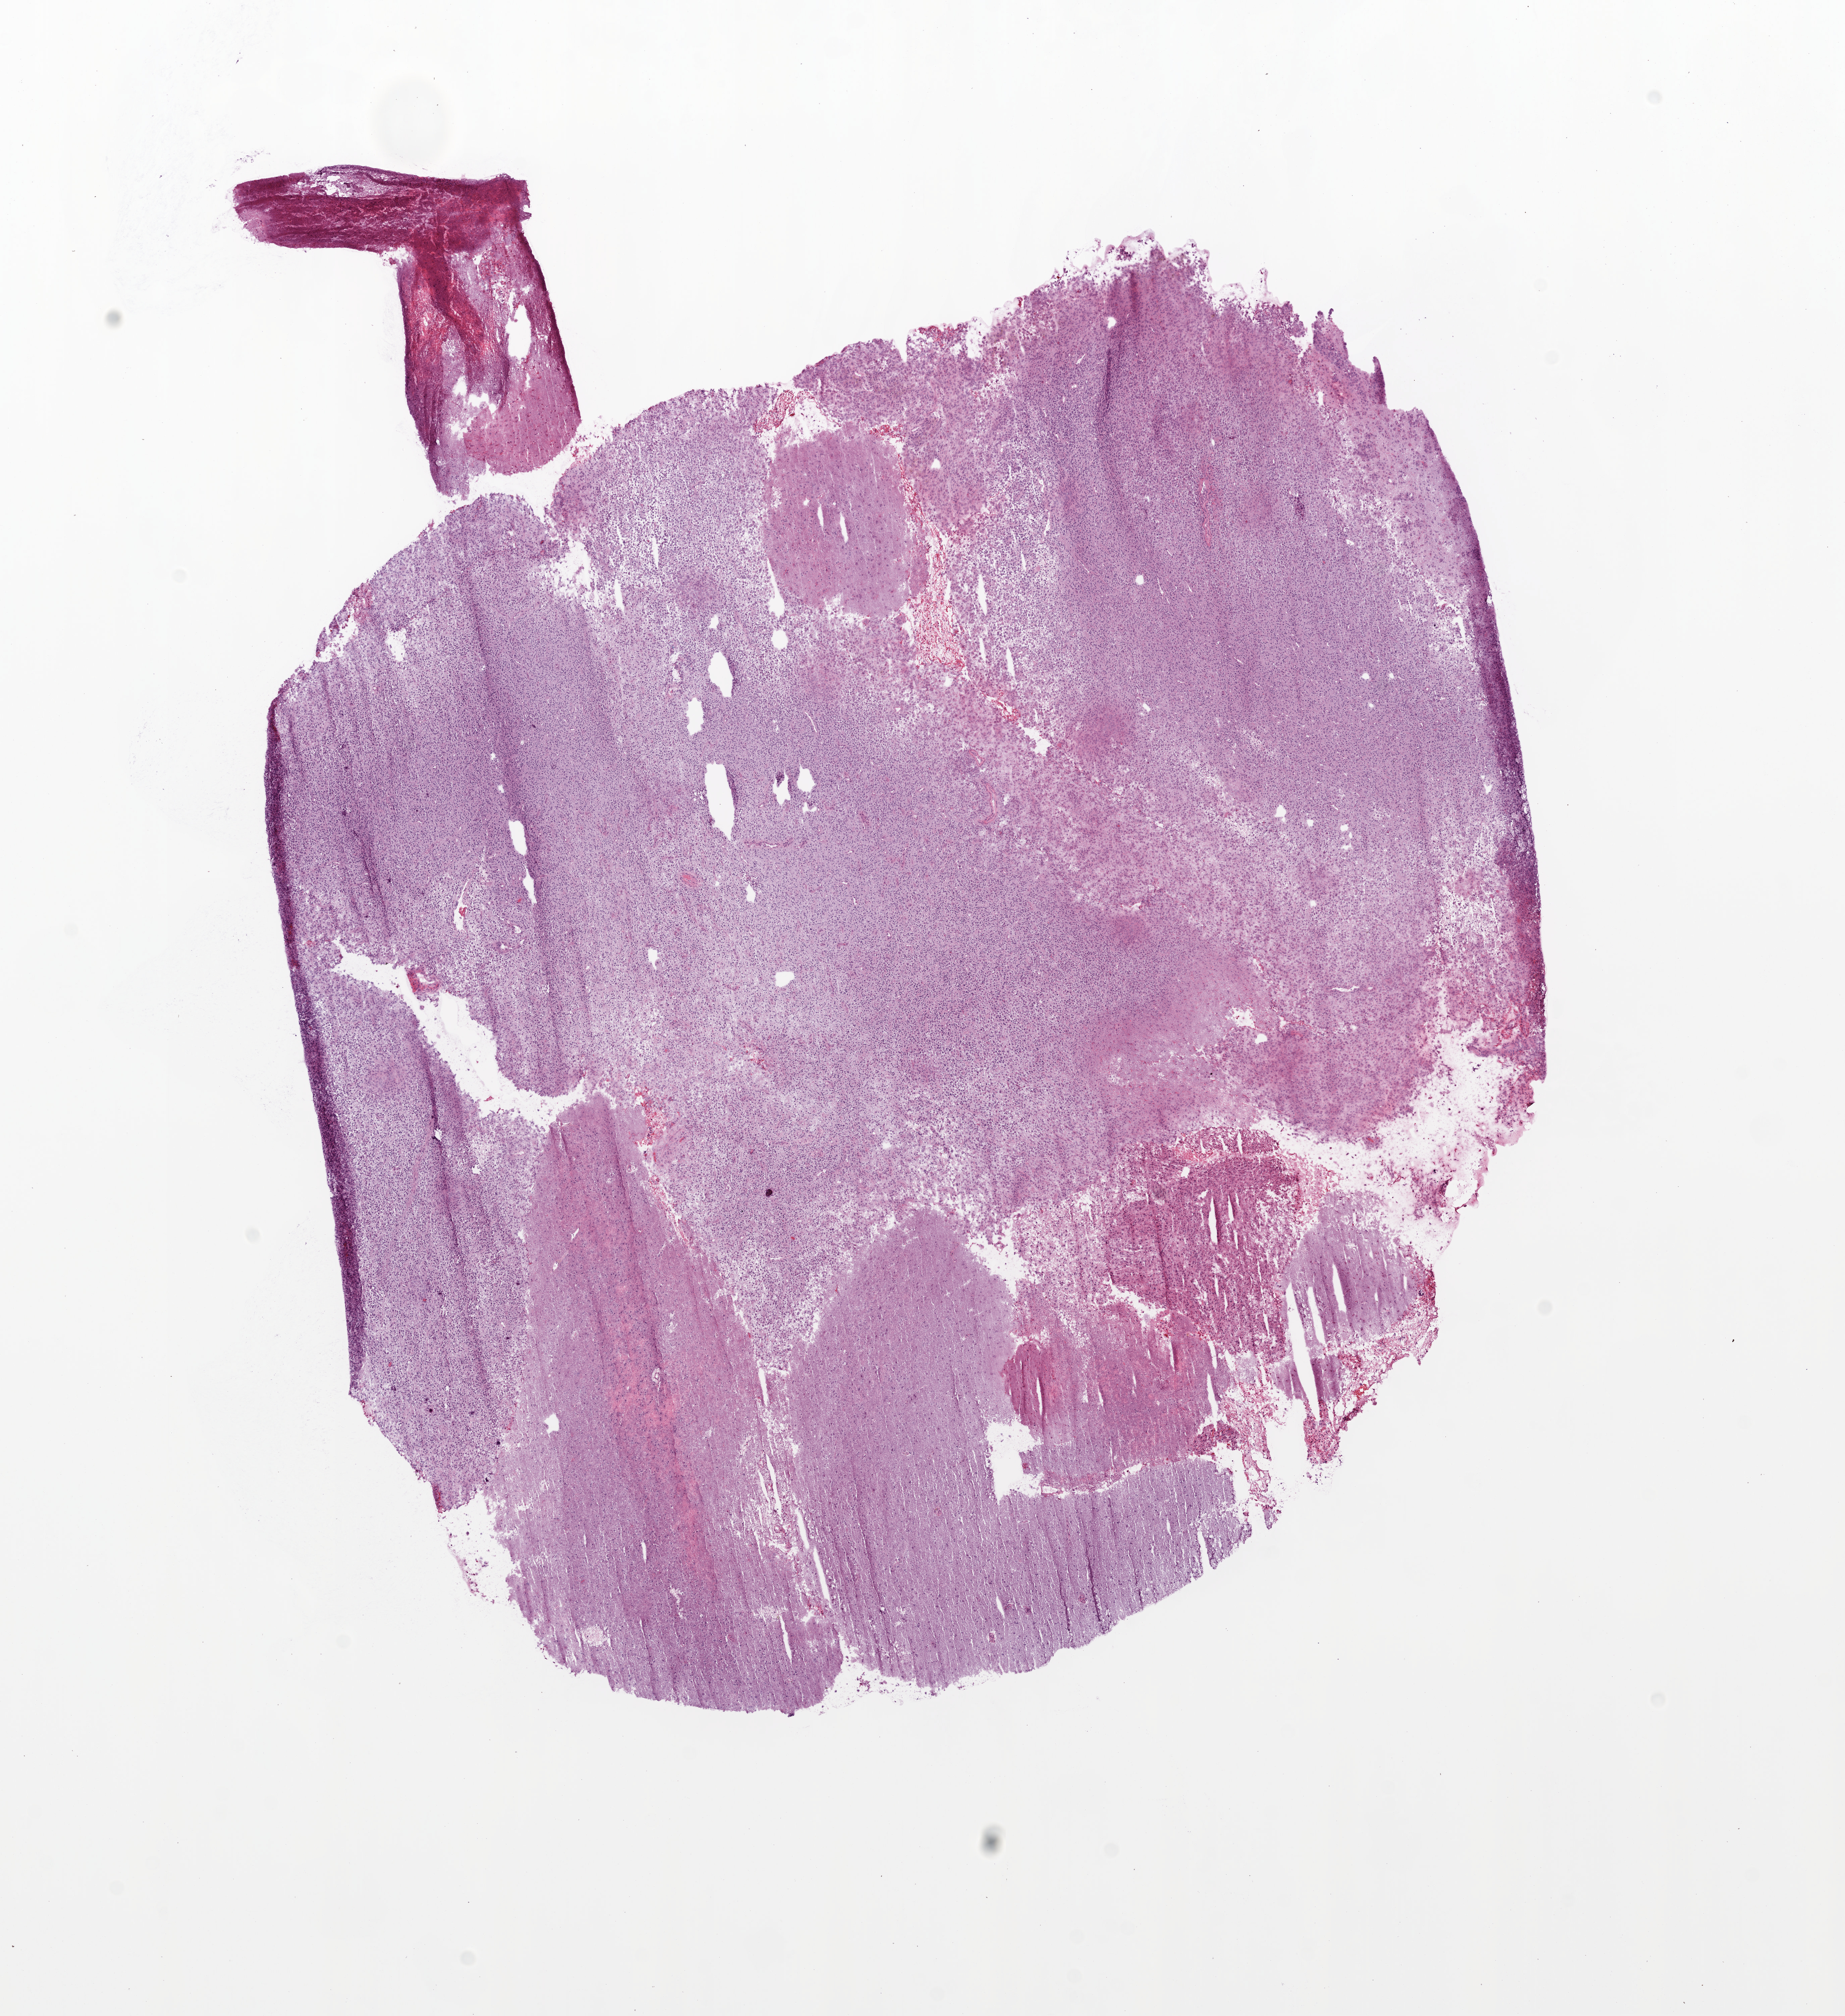
Whole-slide histology image, H&E-stained — shown as a low-resolution overview of the whole scanned area (about 11.0 x 12.1 mm, acquisition: 20x scan). Frozen section from the top of the tissue portion. Brain, primary tumour sample. Female patient; age at initial diagnosis 23 years. Slide review estimates, as recorded: tumour cells 95%, tumour nuclei 85%, normal cells 0%, stromal cells 0%, necrosis 5%.
* histologic diagnosis: Glioblastoma